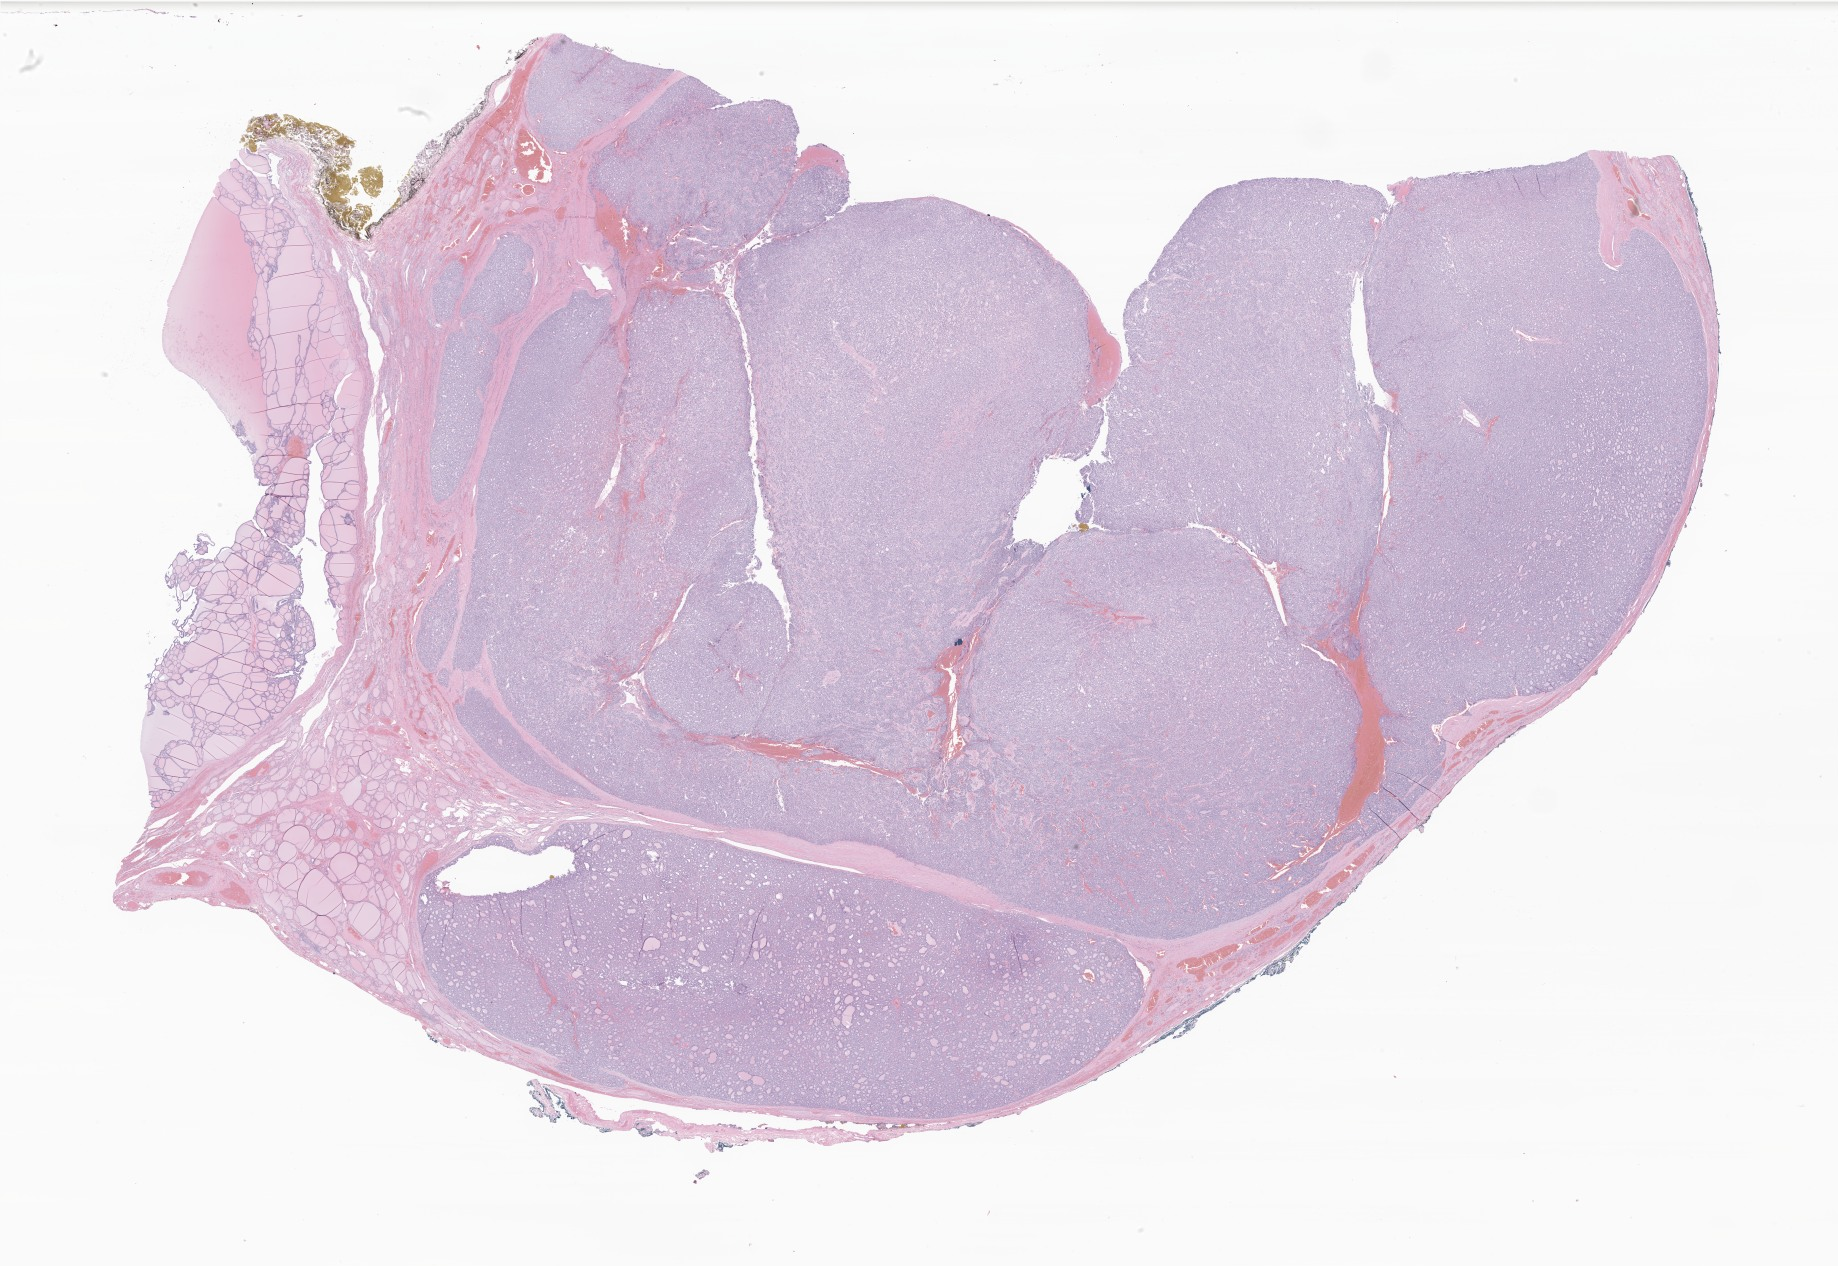
H&E whole-slide image of tumor tissue from the thyroid — whole scanned area (about 31.0 x 21.4 mm) shown as a low-resolution overview, formalin-fixed paraffin-embedded section. Patient female; age 227 months (18 years 11 months).
Diagnosis: Carcinoma, NOS.